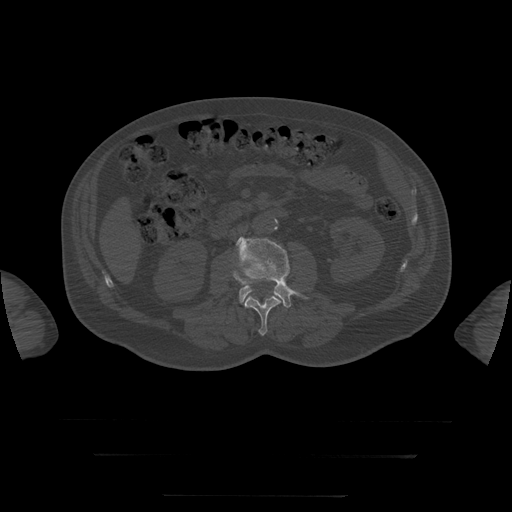
CT including the spine, one axial slice. Slice 10 of 397 in the series (ordered by position). 120 kVp. Bone window (W 1800 / L 400 HU). 1.25 mm slice thickness. 512 × 512 image matrix. Patient age 73 years. Case-level facts recorded for this patient, not image findings: primary cancer: prostate.
Annotated regions visible in this slice (semi-automatic segmentation, software-assisted and operator-edited):
- L3 vertebra: bounding box [x1, y1, x2, y2] px = [236, 237, 300, 308]